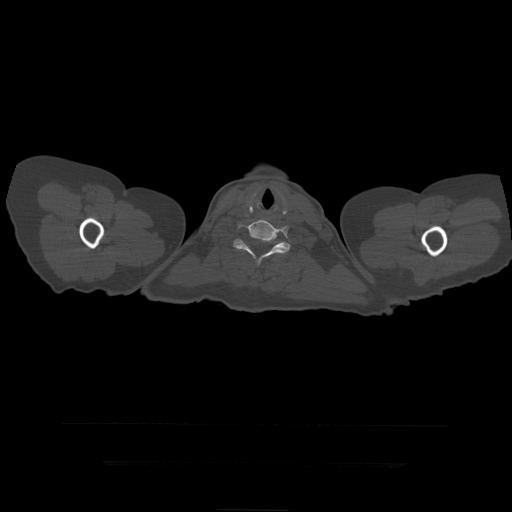
CT including the spine, one axial slice; reconstruction kernel STANDARD; 120 kVp; bone window (W 1800 / L 400 HU); 1.25 mm slice thickness; 512 × 512 image matrix, field of view 450 × 450 mm. Patient age 41 years. Case-level facts recorded for this patient, not image findings: primary cancer: breast.
Structures marked on this image (semi-automatically segmented with operator editing):
- T1 vertebra: bounding box [x1, y1, x2, y2] px = [233, 235, 291, 254]